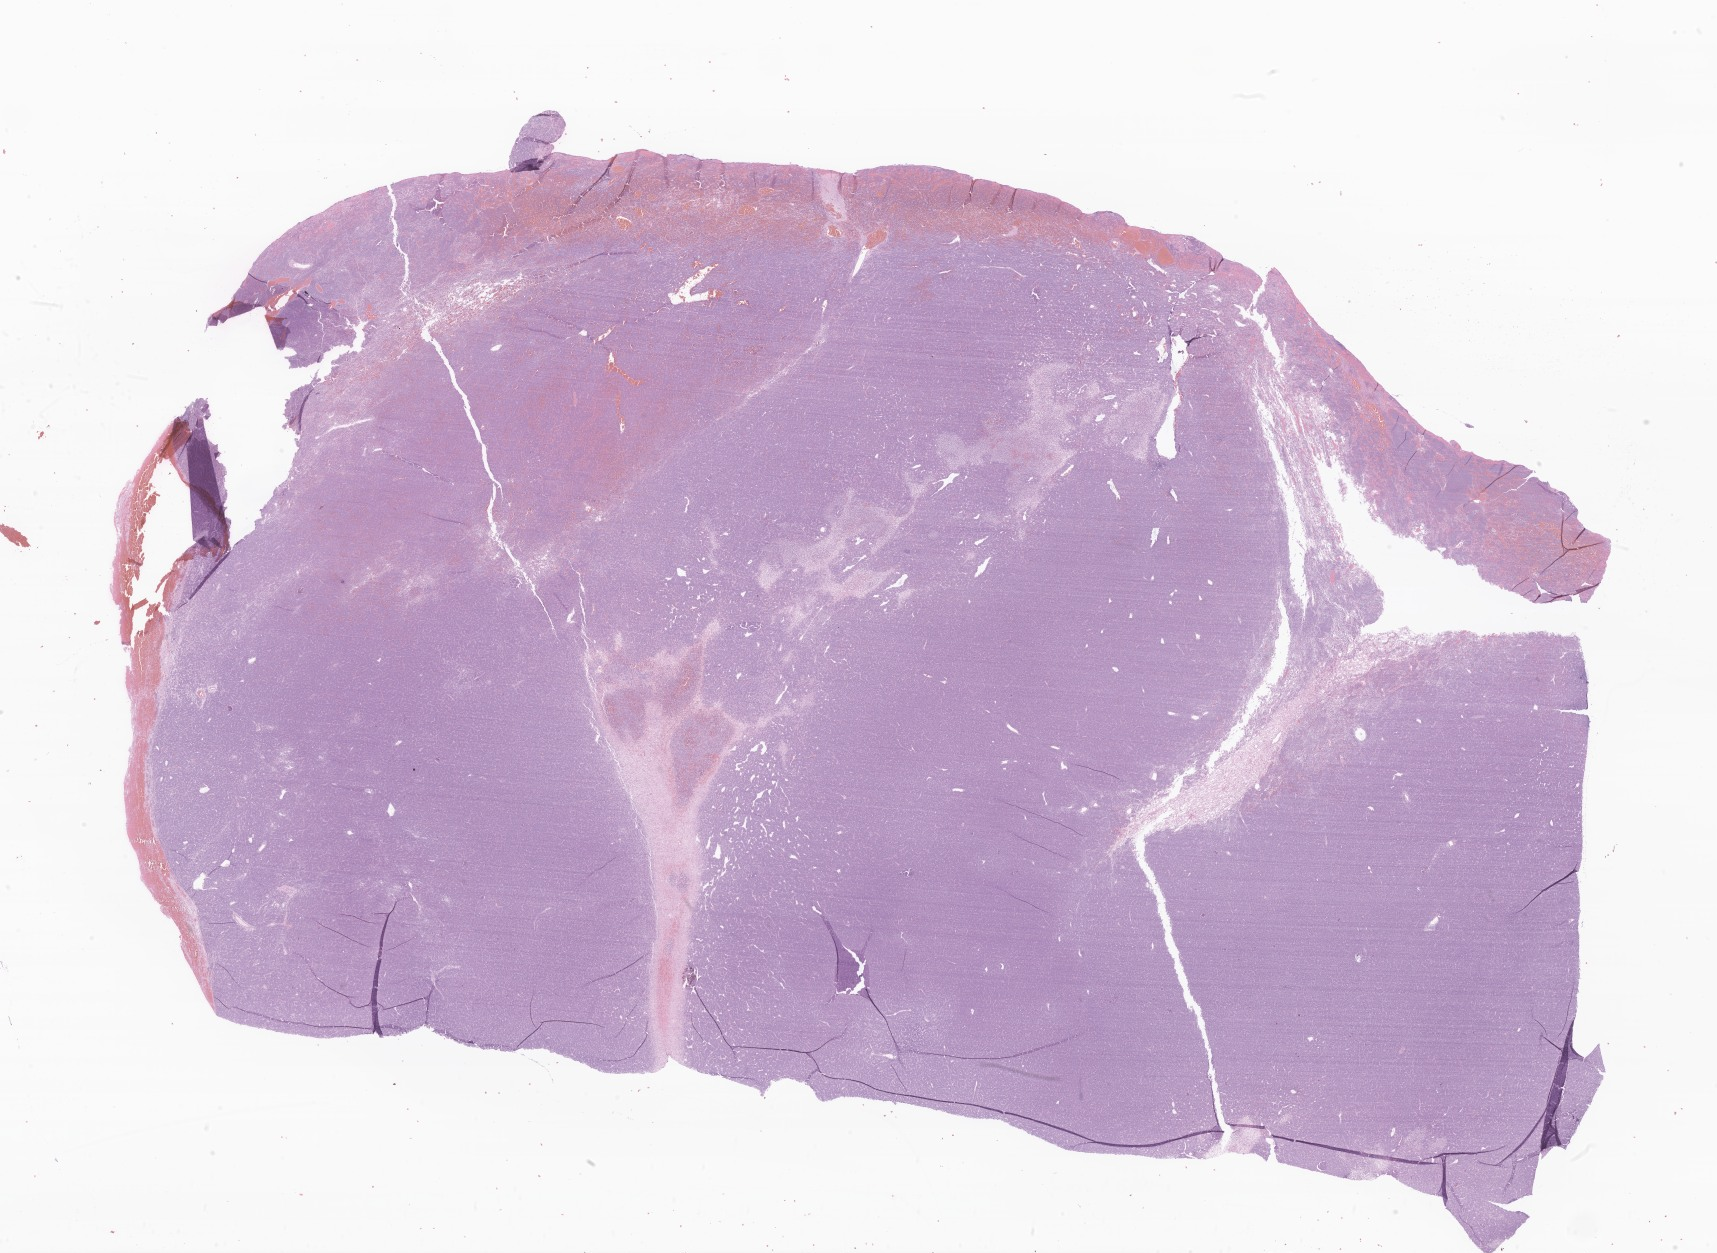
H&E whole-slide image of tumor tissue from the occipital lobe, low-resolution overview of the scanned area, about 29.0 x 21.1 mm, formalin-fixed paraffin-embedded section. Patient: female, age 789 days.
Recorded diagnosis: Myeloid sarcoma.